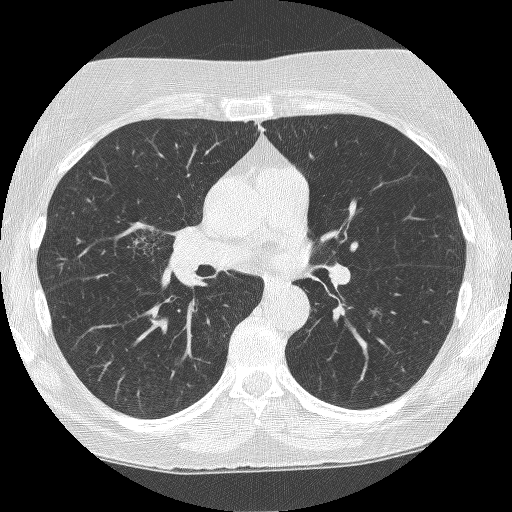
Low-dose screening chest CT, axial slice. Second screening round (one year after baseline). Lung window (W 1500 / L -600 HU). 1.25 mm slice thickness. Slice 135 of 249 in the series. Female participant, aged 64 years at enrolment. Former smoker at enrolment.
Expert-annotated lung lesion, bounding box <116,205,200,286> (left, top, right, bottom; pixels). The screening reader recorded 4 non-calcified nodules or masses ≥4 mm on this exam; which of them this box marks is not recorded. Official screen result: positive, other. Later outcome: lung cancer diagnosed 381 days after this screen — adenocarcinoma, NOS, right upper lobe, right middle lobe, right hilum, stage IV (AJCC 6th edition), 85 mm at pathology.